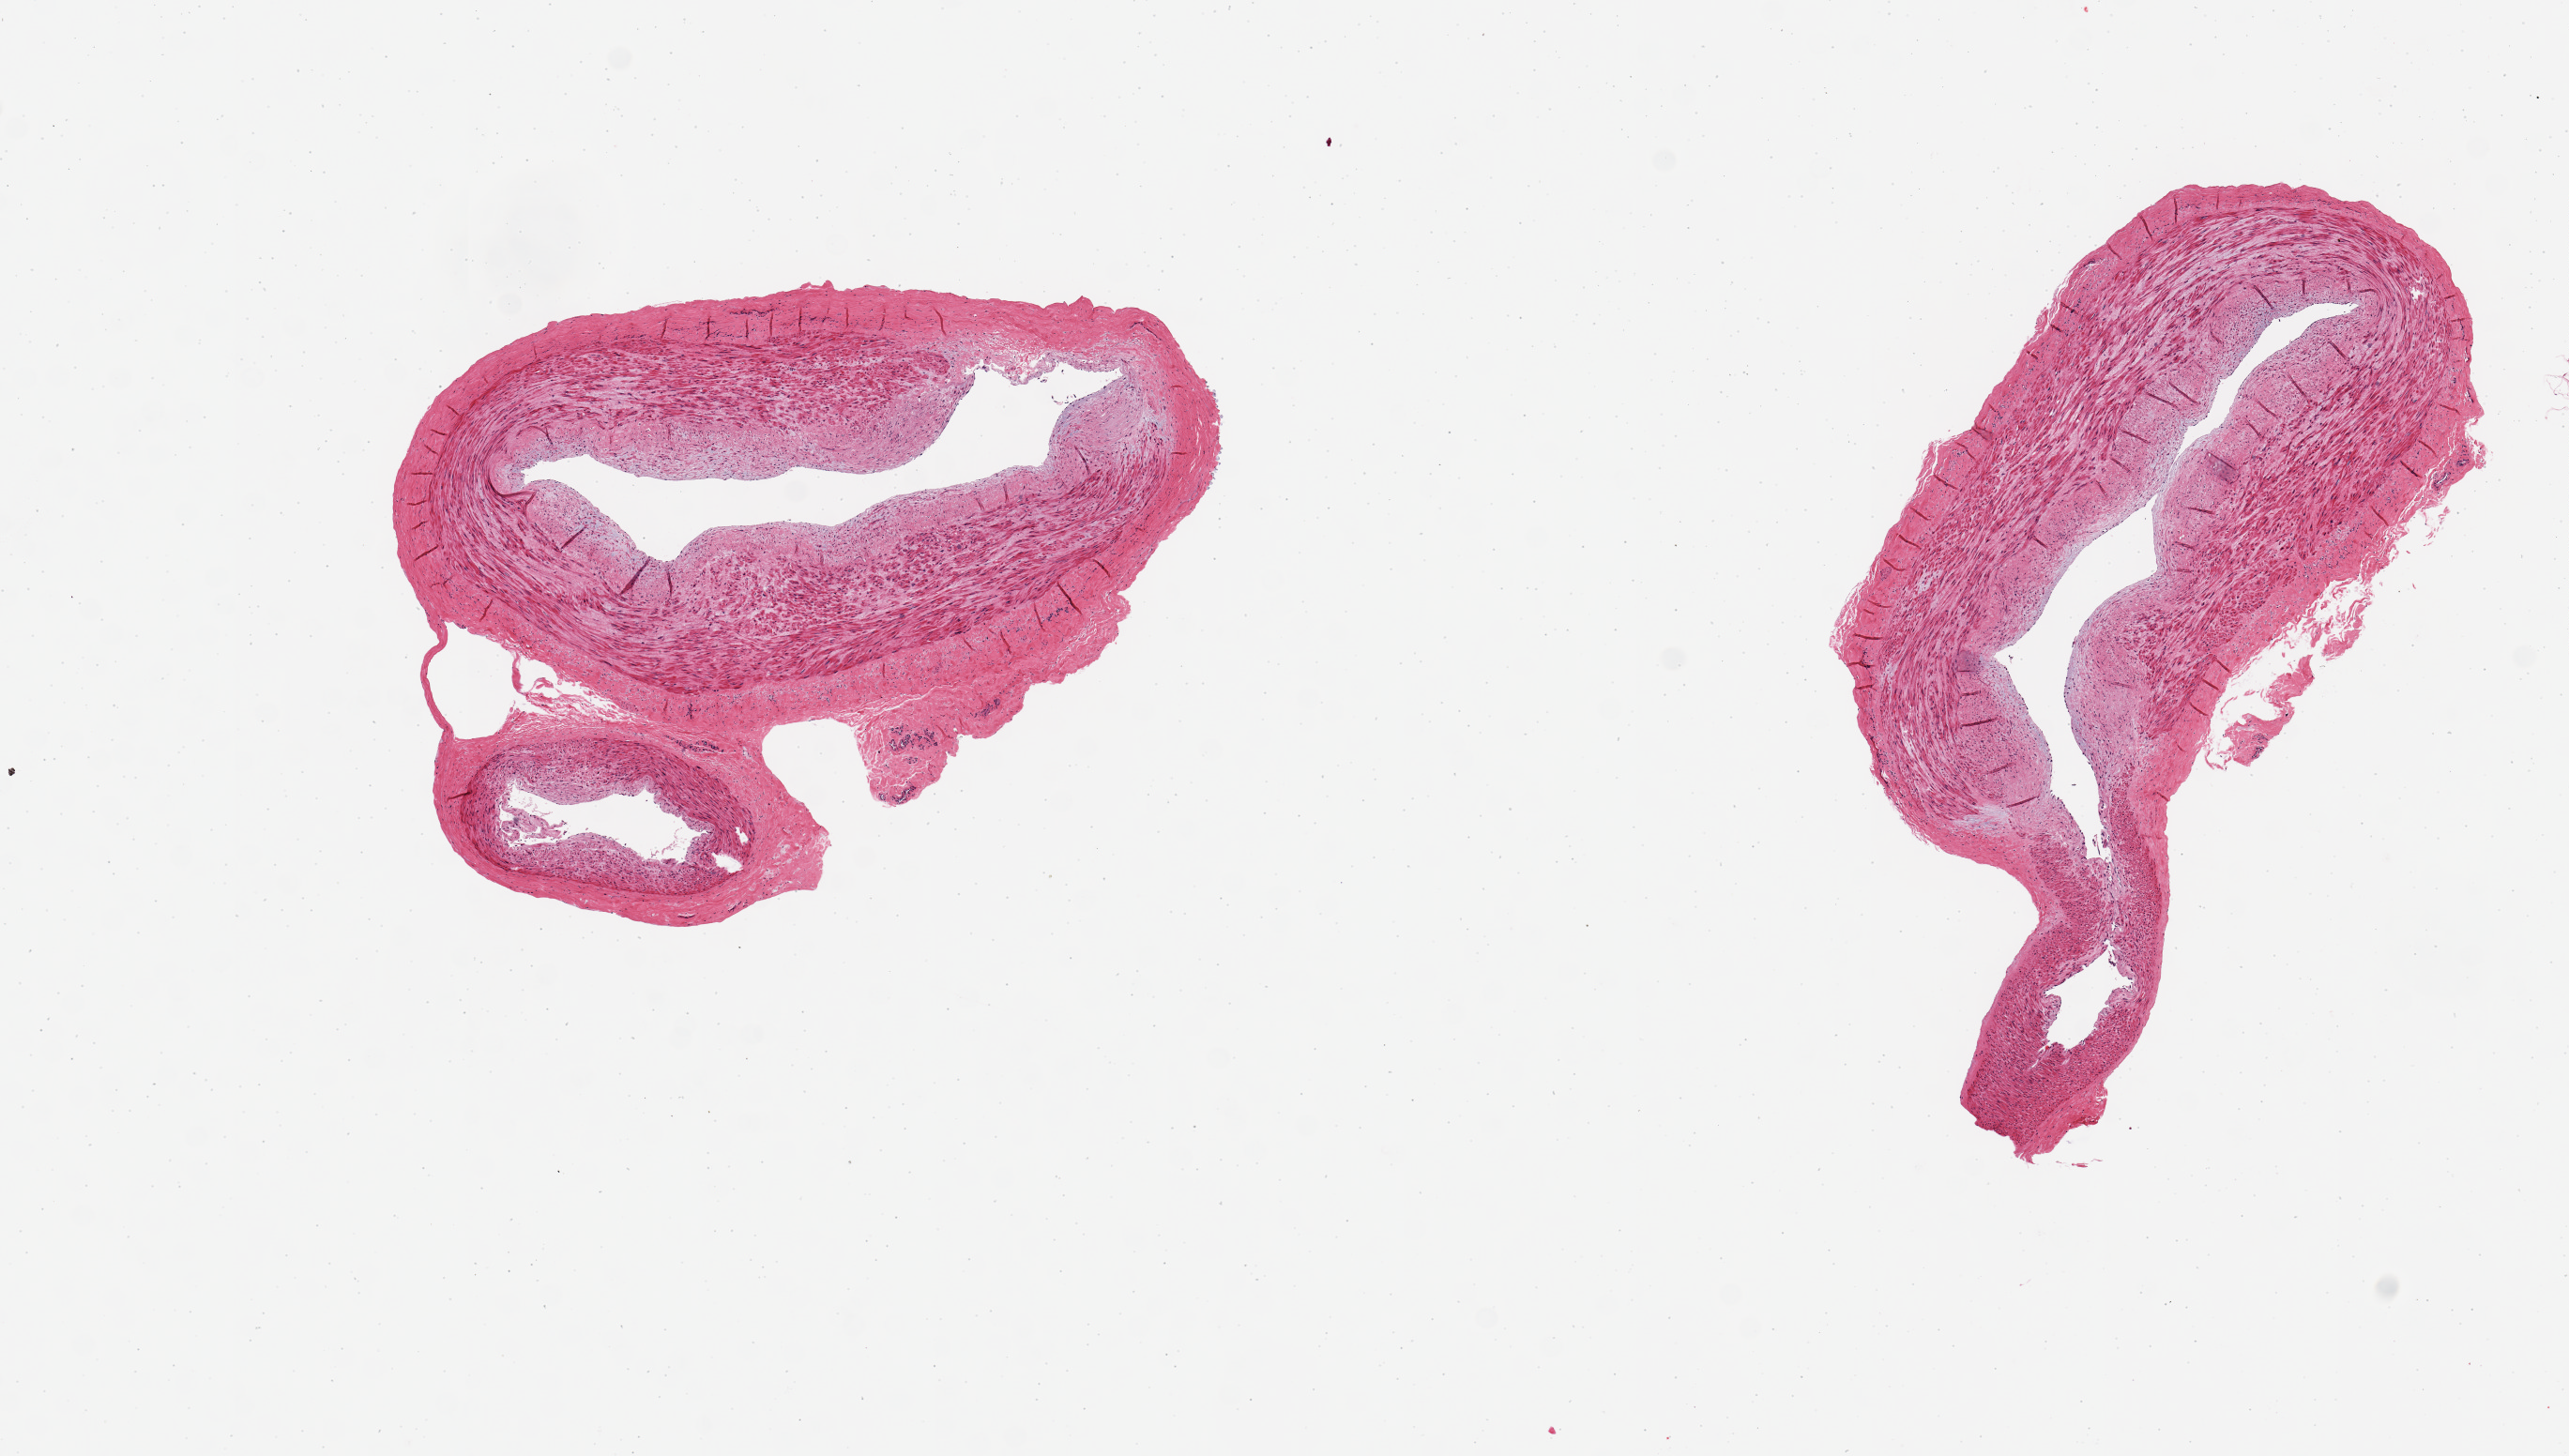
Digitized H&E-stained section — shown as a low-resolution overview of the whole scanned area (about 10.8 x 6.1 mm), PAXgene-fixed paraffin-embedded (PFPE) section, section of tibial artery (target tissue), tissue donor sample. Male donor.
- review note (as recorded): 2 pieces, 3x2.5 & 4x1.8 mm; clean (no adipose tissue); mildly elevated intimal plaques